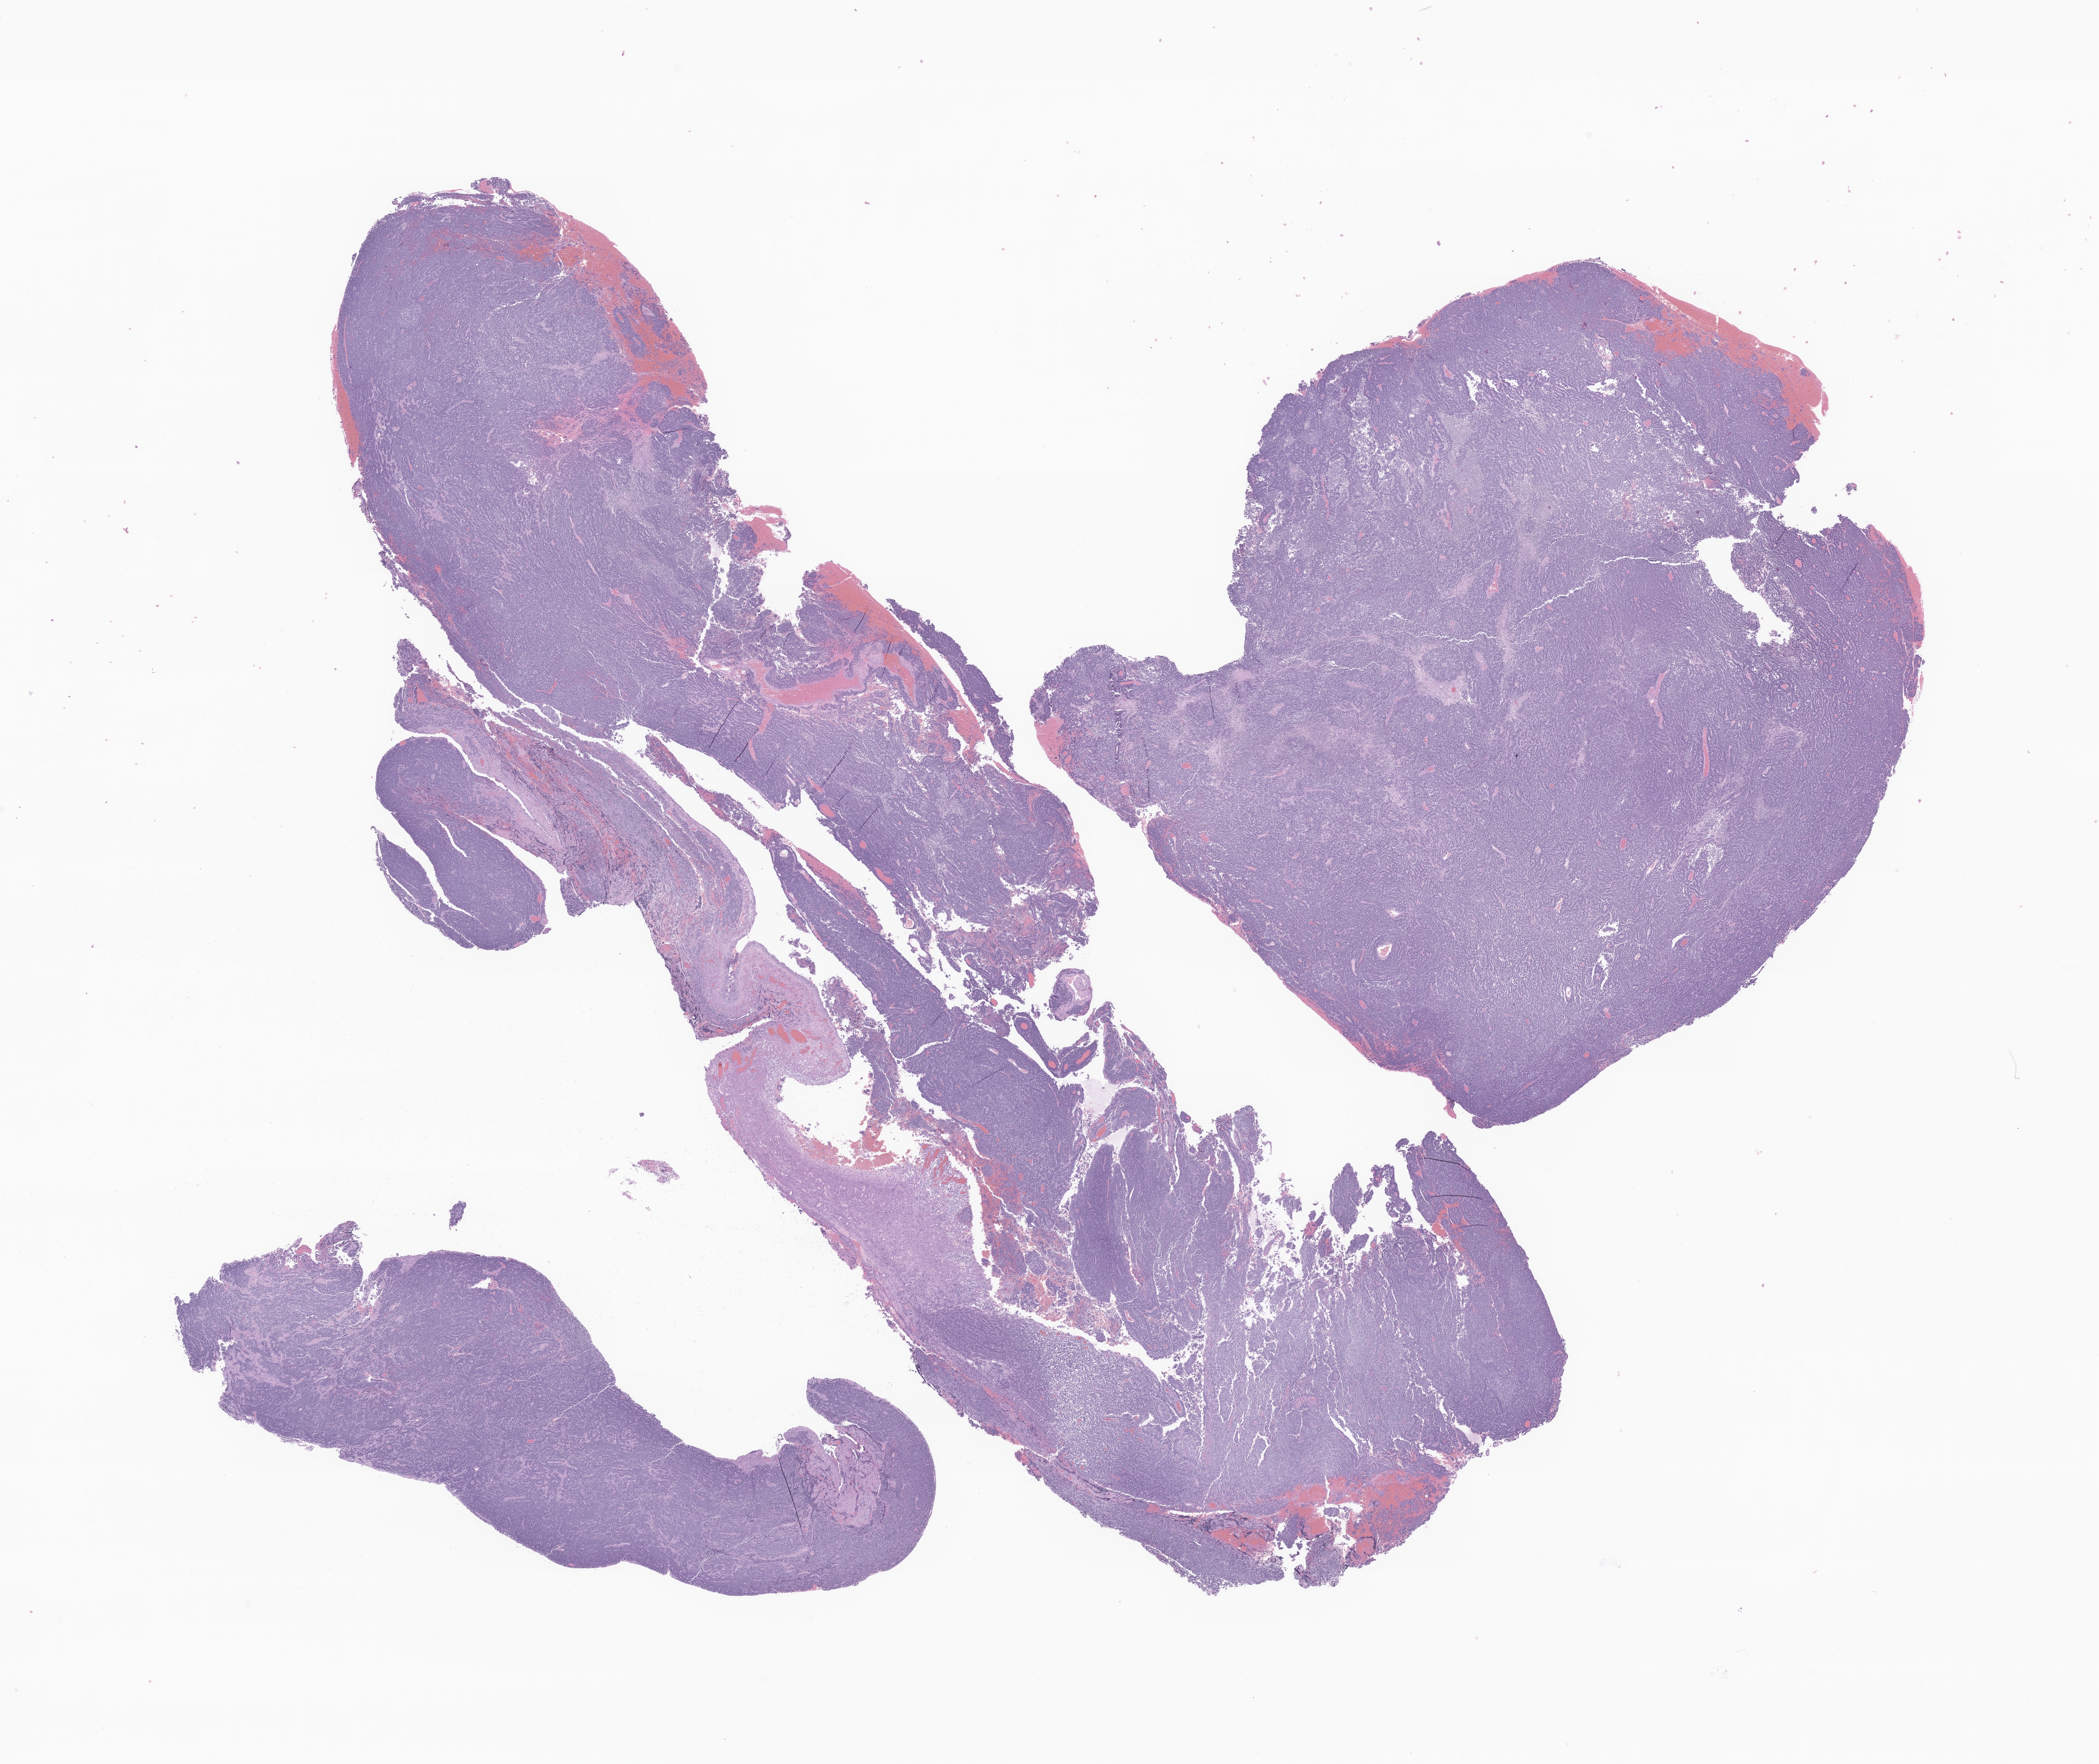
Whole-slide image, H&E stain of tumor tissue from the cerebellum, shown as a low-resolution overview of the whole scanned area (about 22.5 x 18.9 mm). Formalin-fixed paraffin-embedded section. Male patient, age 256 months (21 years 4 months).
Diagnosis: Medulloblastoma, NOS.